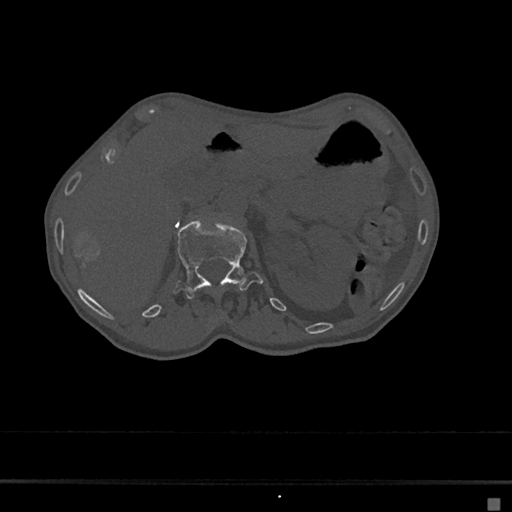
CT including the spine, one axial slice; position 75 of 797 along the scan axis; reconstruction kernel Br40s/3; bone window (W 1800 / L 400 HU); 512 × 512 image matrix. Female patient, age 68 years. From the clinical record (not read from this slice): primary cancer: renal.
Outlined on this slice (semi-automatic segmentation, software-assisted and operator-edited):
- L1 vertebra: bounding box (x1, y1, x2, y2) in pixels: (173, 218, 263, 299)
- T12 vertebra: (214, 315, 222, 325)